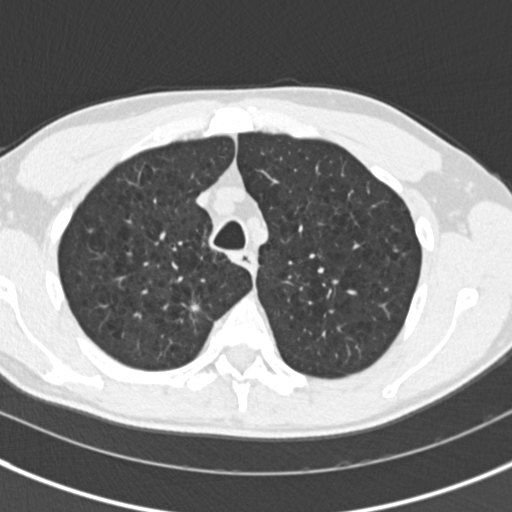
Low-dose screening chest CT, one axial slice; slice 135 of 175 in the series (ordered by position); reconstruction kernel B30f; 120 kVp; lung window (W 1500 / L -600 HU); 512 × 512 image matrix, field of view 306 × 306 mm.
Outlined on this slice (expert manual segmentation):
- lesion 2 (tumor, upper lobe of right lung): bounding box [x1, y1, x2, y2] px = [191, 303, 200, 312]